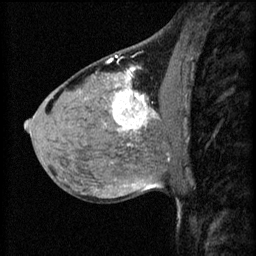
Breast MRI (dynamic contrast-enhanced), one sagittal slice. Position 33 of 60 along the scan axis. 3 images stored at this slice position (order not interpretable as contrast timing). 1.5 T. TE 4.2 ms, TR 8.2 ms. 256 × 256 image matrix. Patient: female, 40 years.
Structures marked on this image (semi-automatic segmentation, software-assisted and operator-edited):
- analysis volume of interest (the breast-tissue region the enhancement analysis was run in; not a lesion): bounding box (x1, y1, x2, y2) in pixels: (108, 82, 175, 139)
- tumour enhancement mask (voxels above the 70 % enhancement threshold inside the analysis volume of interest): (112, 82, 159, 133)